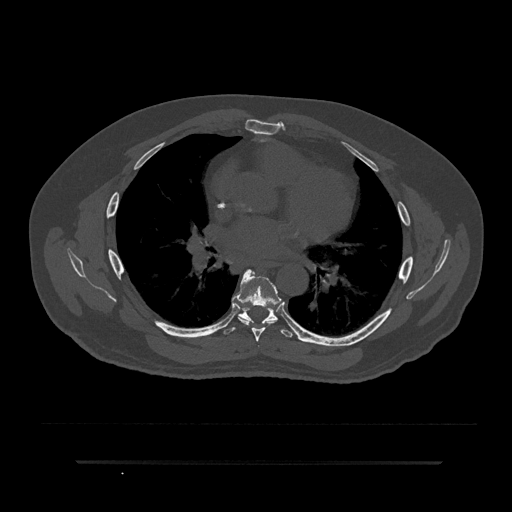
CT including the spine, one axial slice; slice 507 of 797 in the series (ordered by position); reconstruction kernel Br40s/3; 120 kVp; bone window (W 1800 / L 400 HU); 0.5 mm slice thickness; 512 × 512 image matrix, field of view 464 × 464 mm. Patient: male, 59 years. From the clinical record (not read from this slice): primary cancer: bile ducts.
Outlined on this slice (semi-automatic segmentation, software-assisted and operator-edited):
- T6 vertebra: box from (x=232, y=269) to (x=282, y=342) px
- T7 vertebra: (x=223, y=306)–(x=295, y=338)